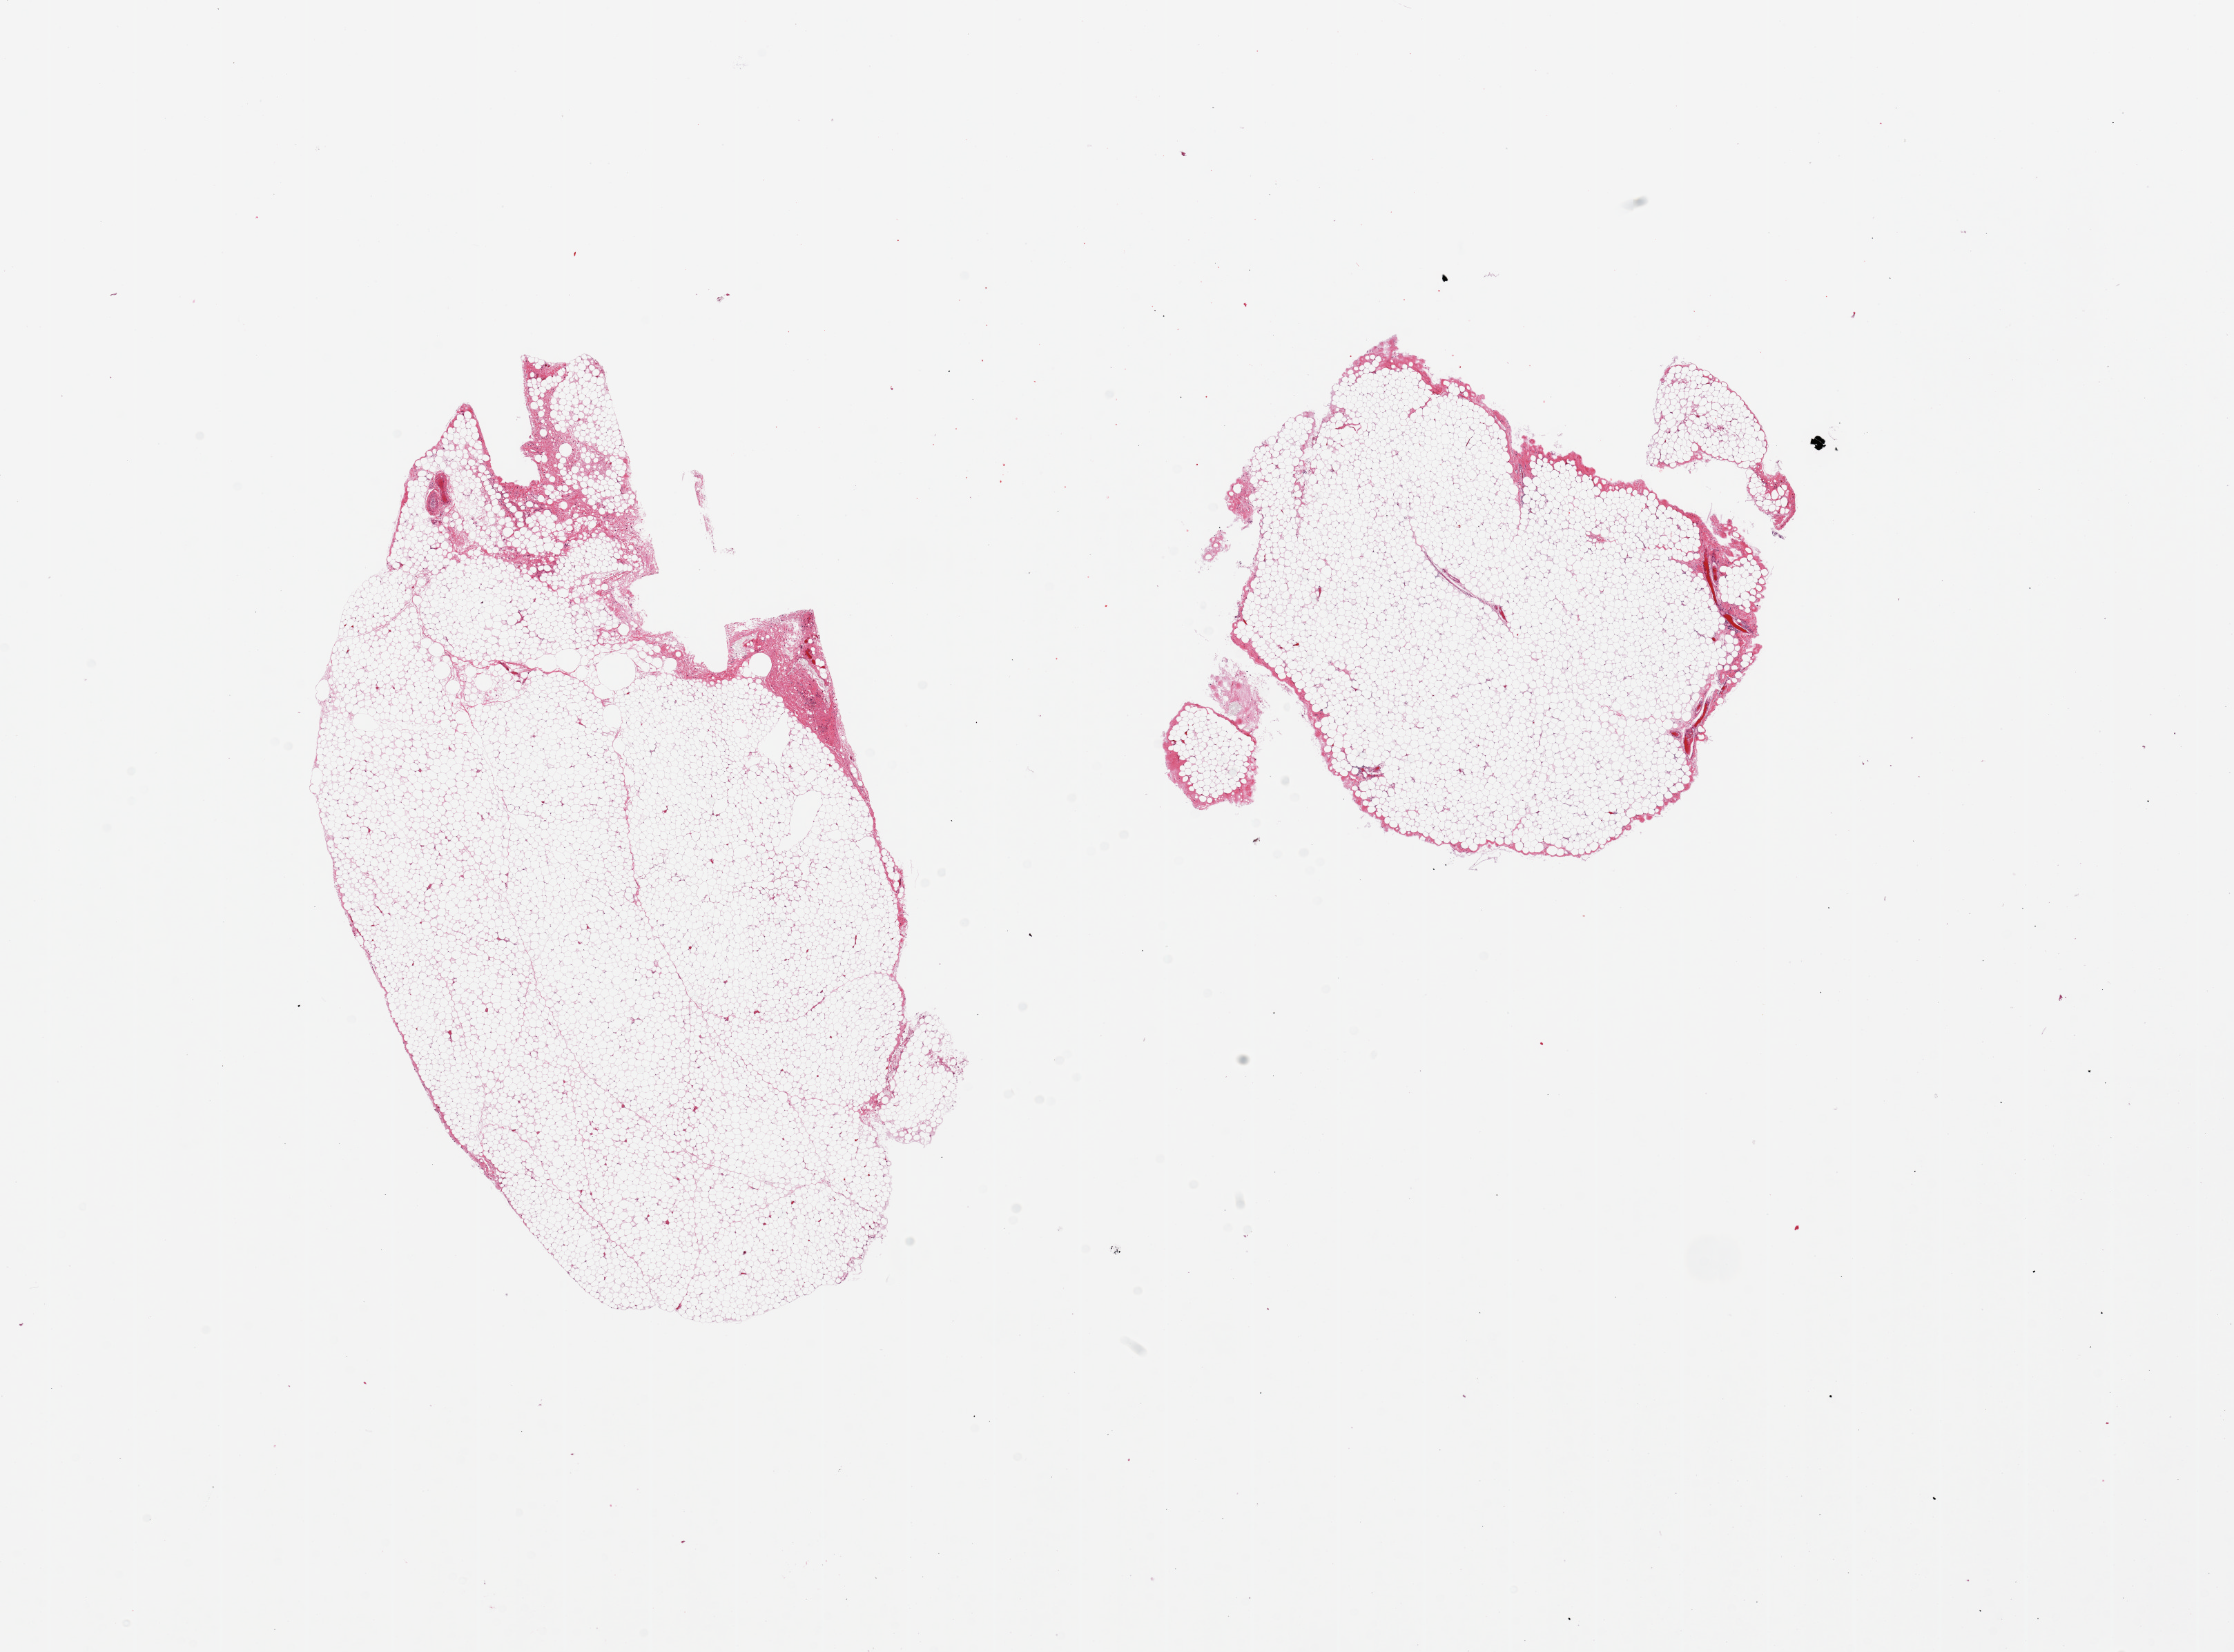
Digitized hematoxylin and eosin (H&E)-stained section — shown as a low-resolution overview of the whole scanned area (about 25.6 x 18.9 mm); PAXgene-fixed paraffin-embedded (PFPE) section; section of pancreas (target tissue); tissue donor sample. Female donor.
* pathologist's review note for this sample: 2 pieces; all adipose tissue, no pancreatic parenchyma is present